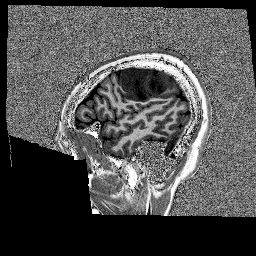
Brain MRI from a brain-tumour surgery series, one sagittal slice; slice 37 of 176 in the series (ordered by position); 1 mm slice thickness; 256 × 256 image matrix, field of view 256 × 256 mm. From the clinical record (not read from this slice): histopathology: Glioblastoma; WHO grade: 4; IDH mutation: no; tumour location: Left Frontal.
Outlined on this slice (manually delineated by an expert):
- tumour: box from (x=118, y=66) to (x=175, y=101) px